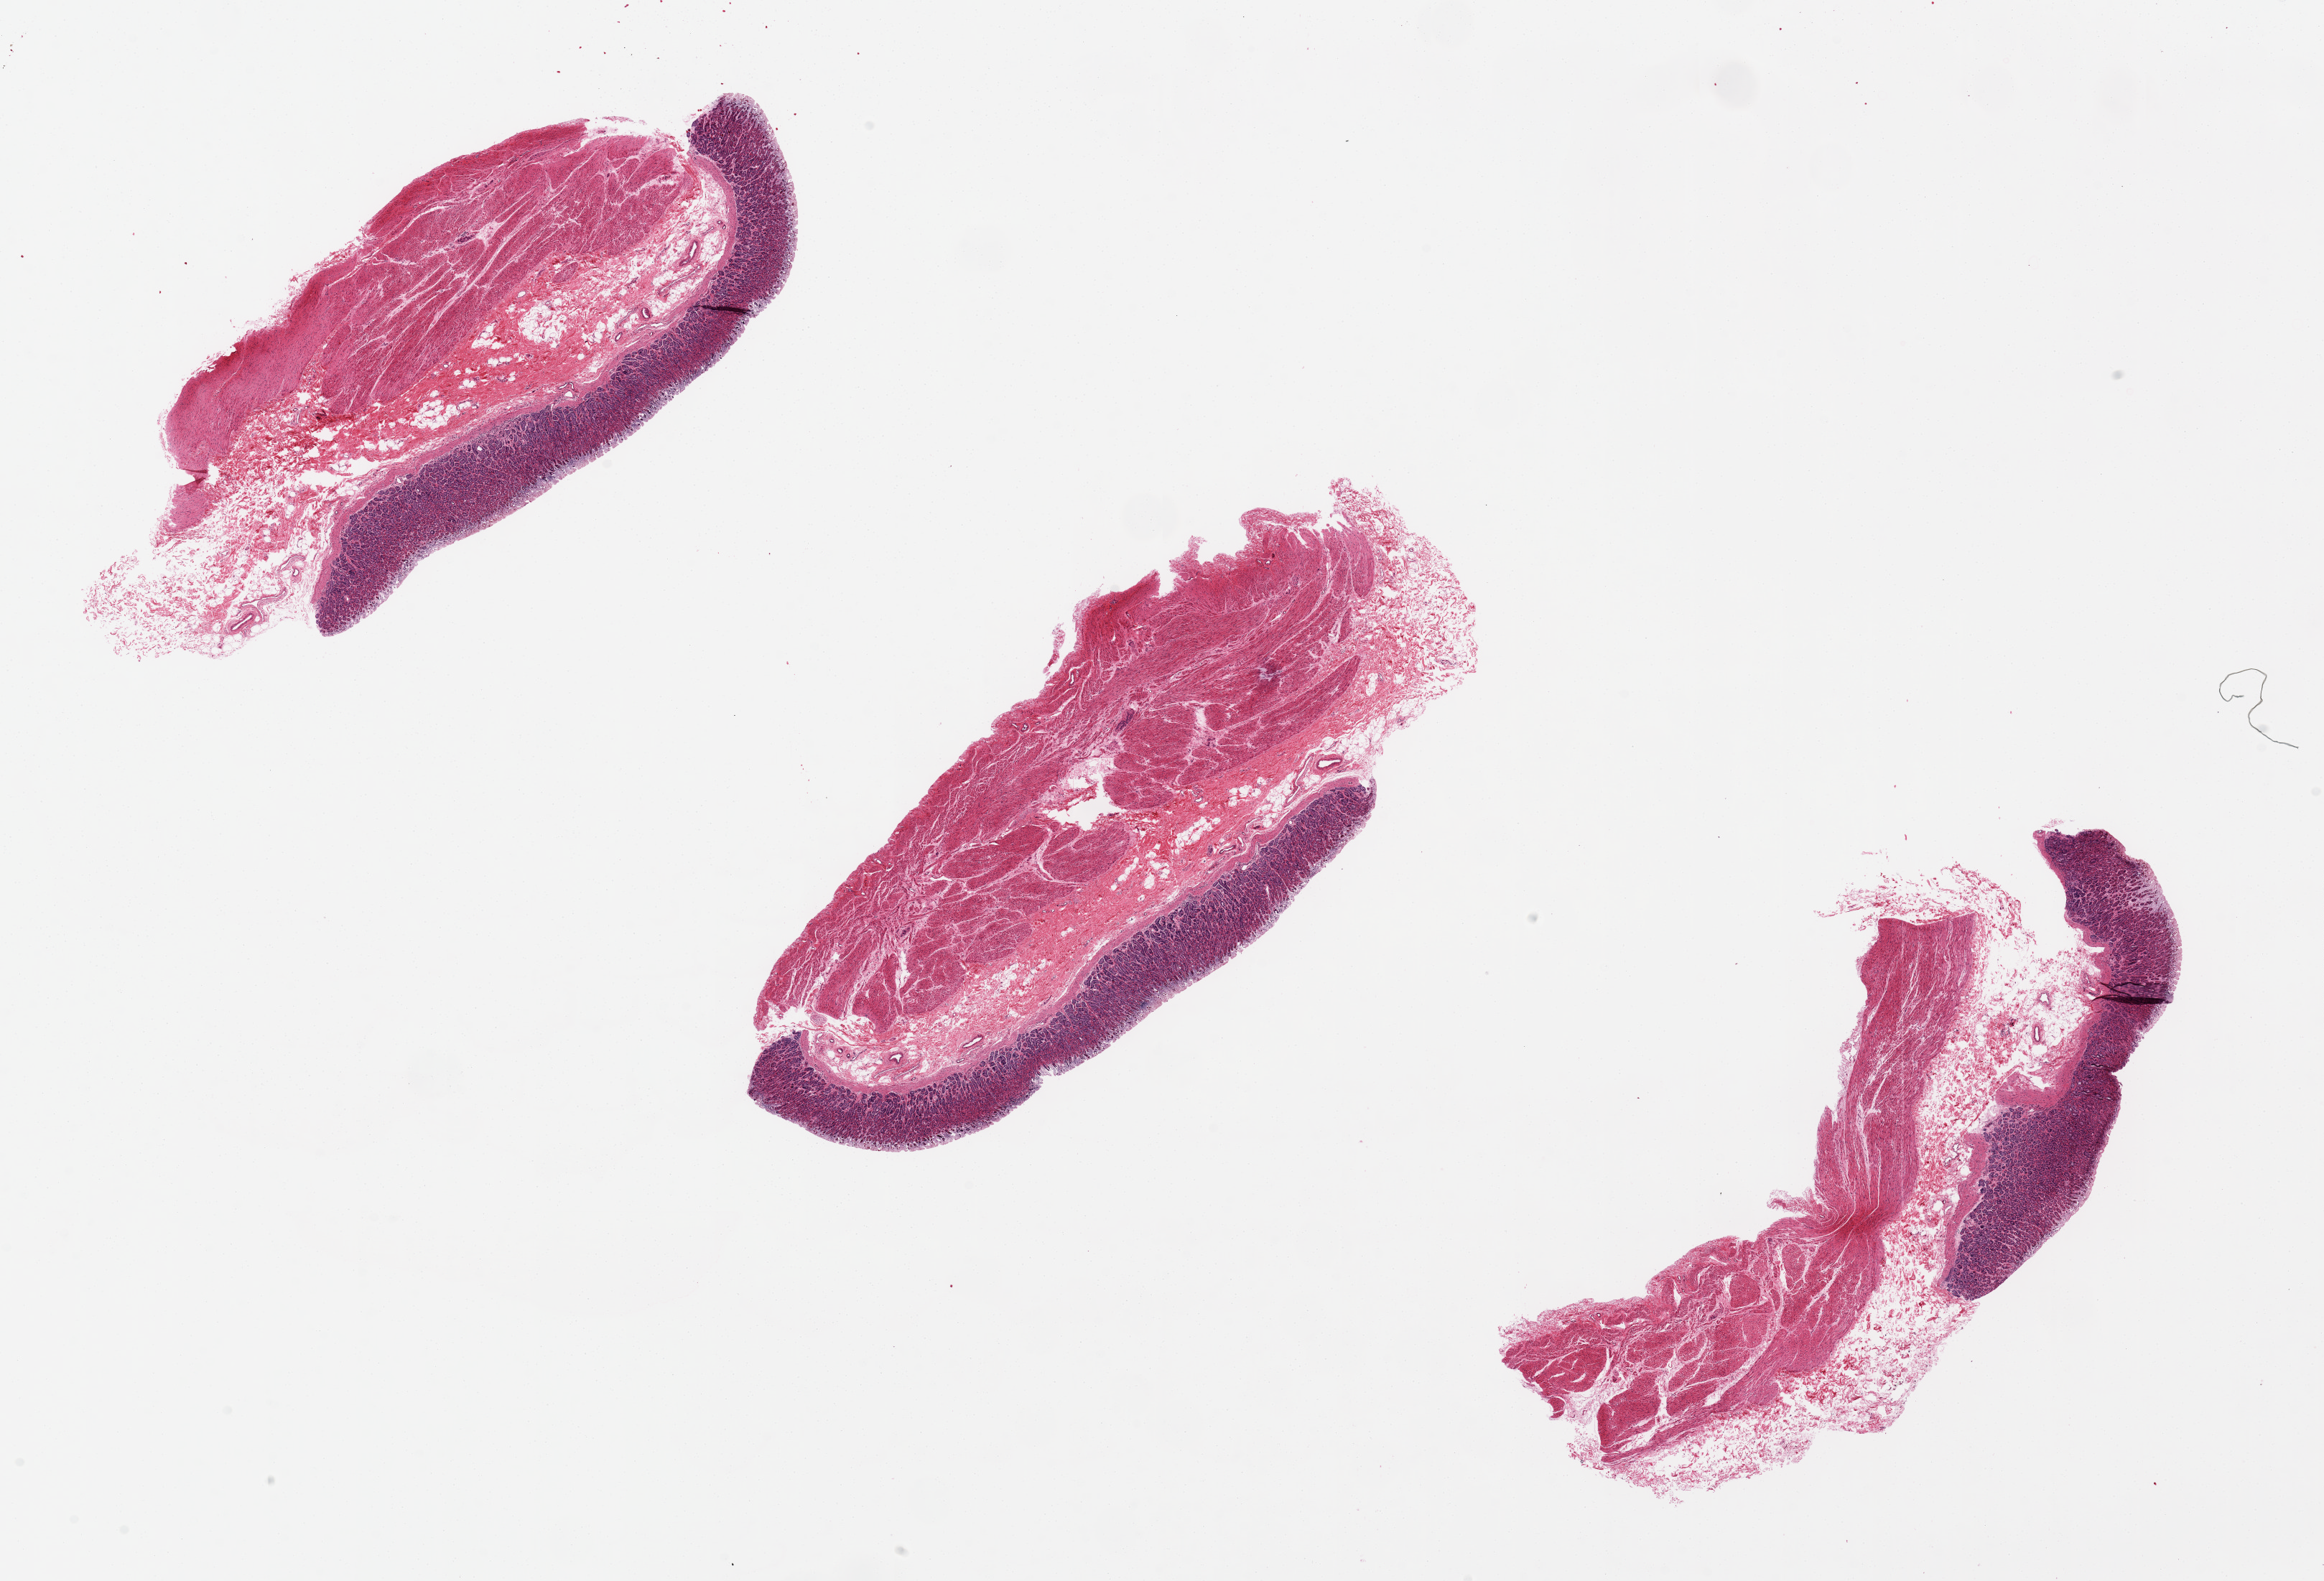
Haematoxylin and eosin whole-slide image, low-resolution overview of the scanned area, about 25.6 x 17.4 mm. PAXgene-fixed paraffin-embedded (PFPE) section. Target tissue: stomach. Tissue donor sample. Donor sex: male.
- reviewer comment on this tissue sample: 1. ~3x8mm pieces; mucosa is ~25% of specimen thickness. Overall epithelium is well-preserved though luminal surface is autolyzed